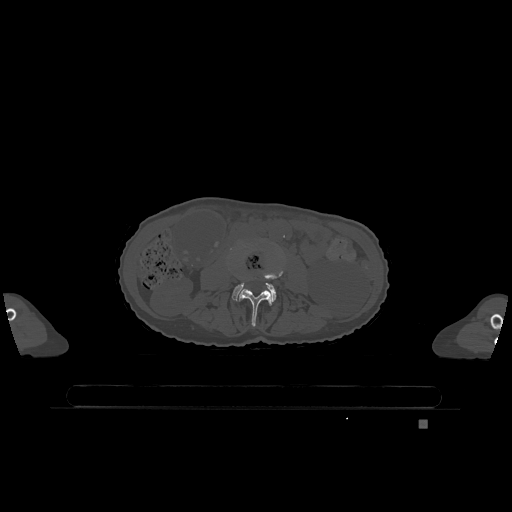
CT including the spine, one axial slice. Slice 339 of 1317 in the series (ordered by position). Bone window (W 1800 / L 400 HU). 512 × 512 image matrix, field of view 500 × 500 mm. Patient: female, 74 years. Case-level facts recorded for this patient, not image findings: primary cancer: lung; vertebrae with lytic lesions (as recorded): T1, T4, T5, T6, L4, L5.
Annotated regions visible in this slice (semi-automatically segmented with operator editing):
- L3 vertebra: bounding box (x1, y1, x2, y2) in pixels: (238, 270, 284, 326)
- L4 vertebra: (232, 282, 277, 302)